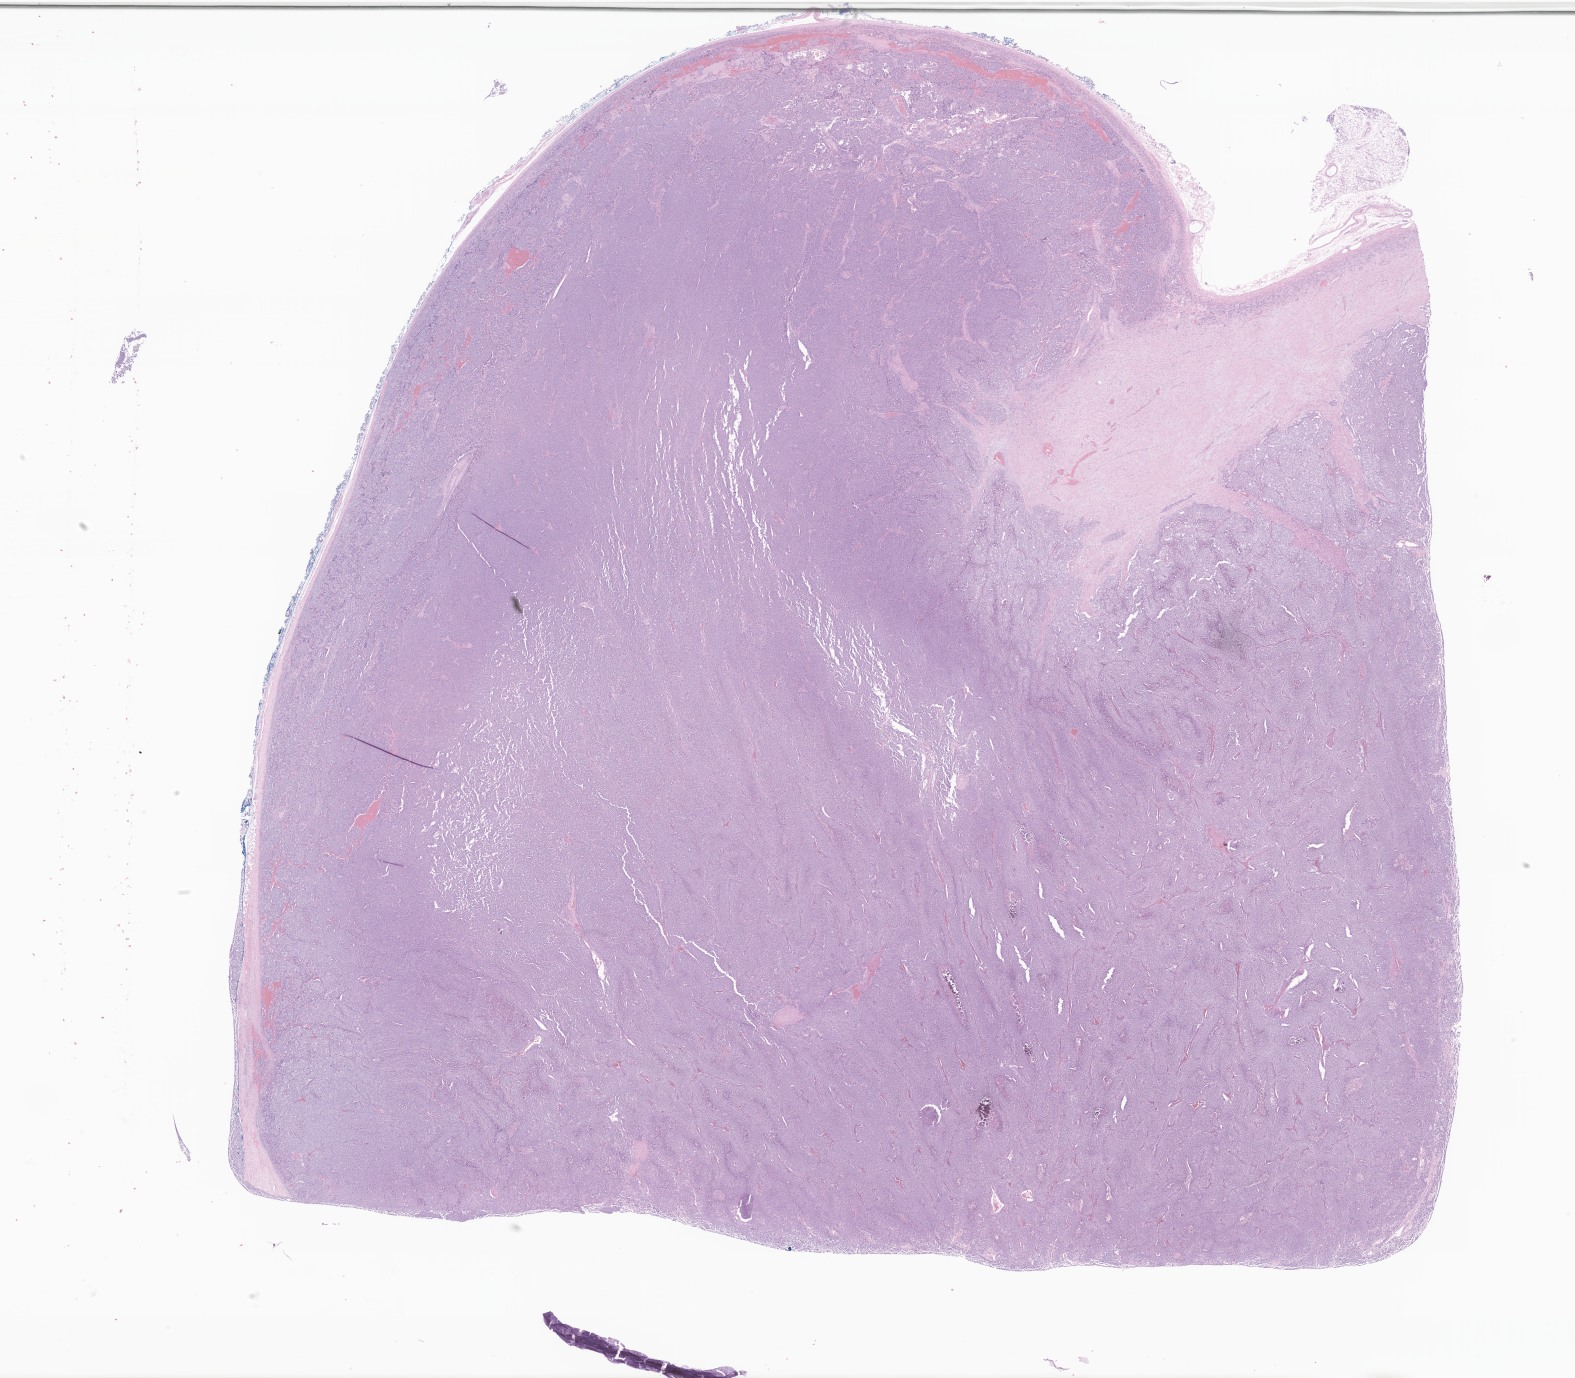
Hematoxylin and eosin (H&E) whole-slide image of tumor tissue from the adrenal gland — low-resolution overview of the scanned area, about 26.6 x 23.2 mm. FFPE section. Male patient, age 142 months (11 years 10 months).
Recorded diagnosis: Neoplasm, malignant.